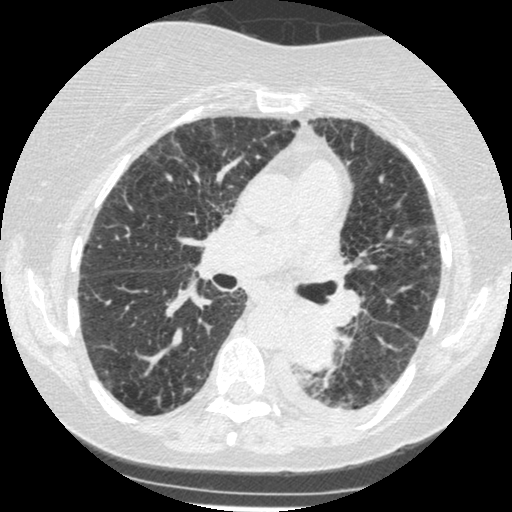
Low-dose screening chest CT, axial slice. Third annual screen. Lung window (W 1500 / L -600 HU). 120 kVp. Female, age 60 years at enrolment. Former smoker at enrolment.
• Lesion marked by an expert reader, box from (x=271, y=307) to (x=342, y=374) px.
• Reader record for this screening exam (exam-level; its link to the box is not recorded): non-calcified nodule or mass ≥4 mm, left lower lobe, 54 × 38 mm, smooth margins, soft tissue attenuation, pre-existing on the prior screen: yes; interval growth: yes.